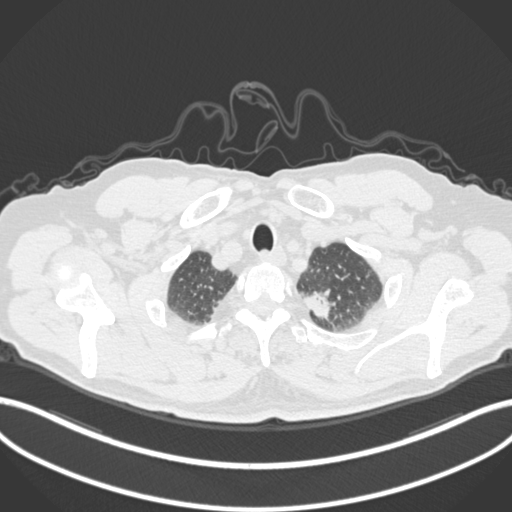
Chest CT, one axial slice. Position 289 of 306 along the scan axis. Reconstruction kernel B30f. 120 kVp. Lung window (W 1500 / L -600 HU). 1 mm slice thickness. 512 × 512 image matrix, field of view 400 × 400 mm. Patient: male, 64 years. From the clinical record (not read from this slice): clinical TNM (as recorded): T1c N0 M0.
Outlined on this slice (bounding box drawn by a radiologist):
- lung tumour (recorded histology: adenocarcinoma): bounding box [x1, y1, x2, y2] px = [298, 286, 335, 321]